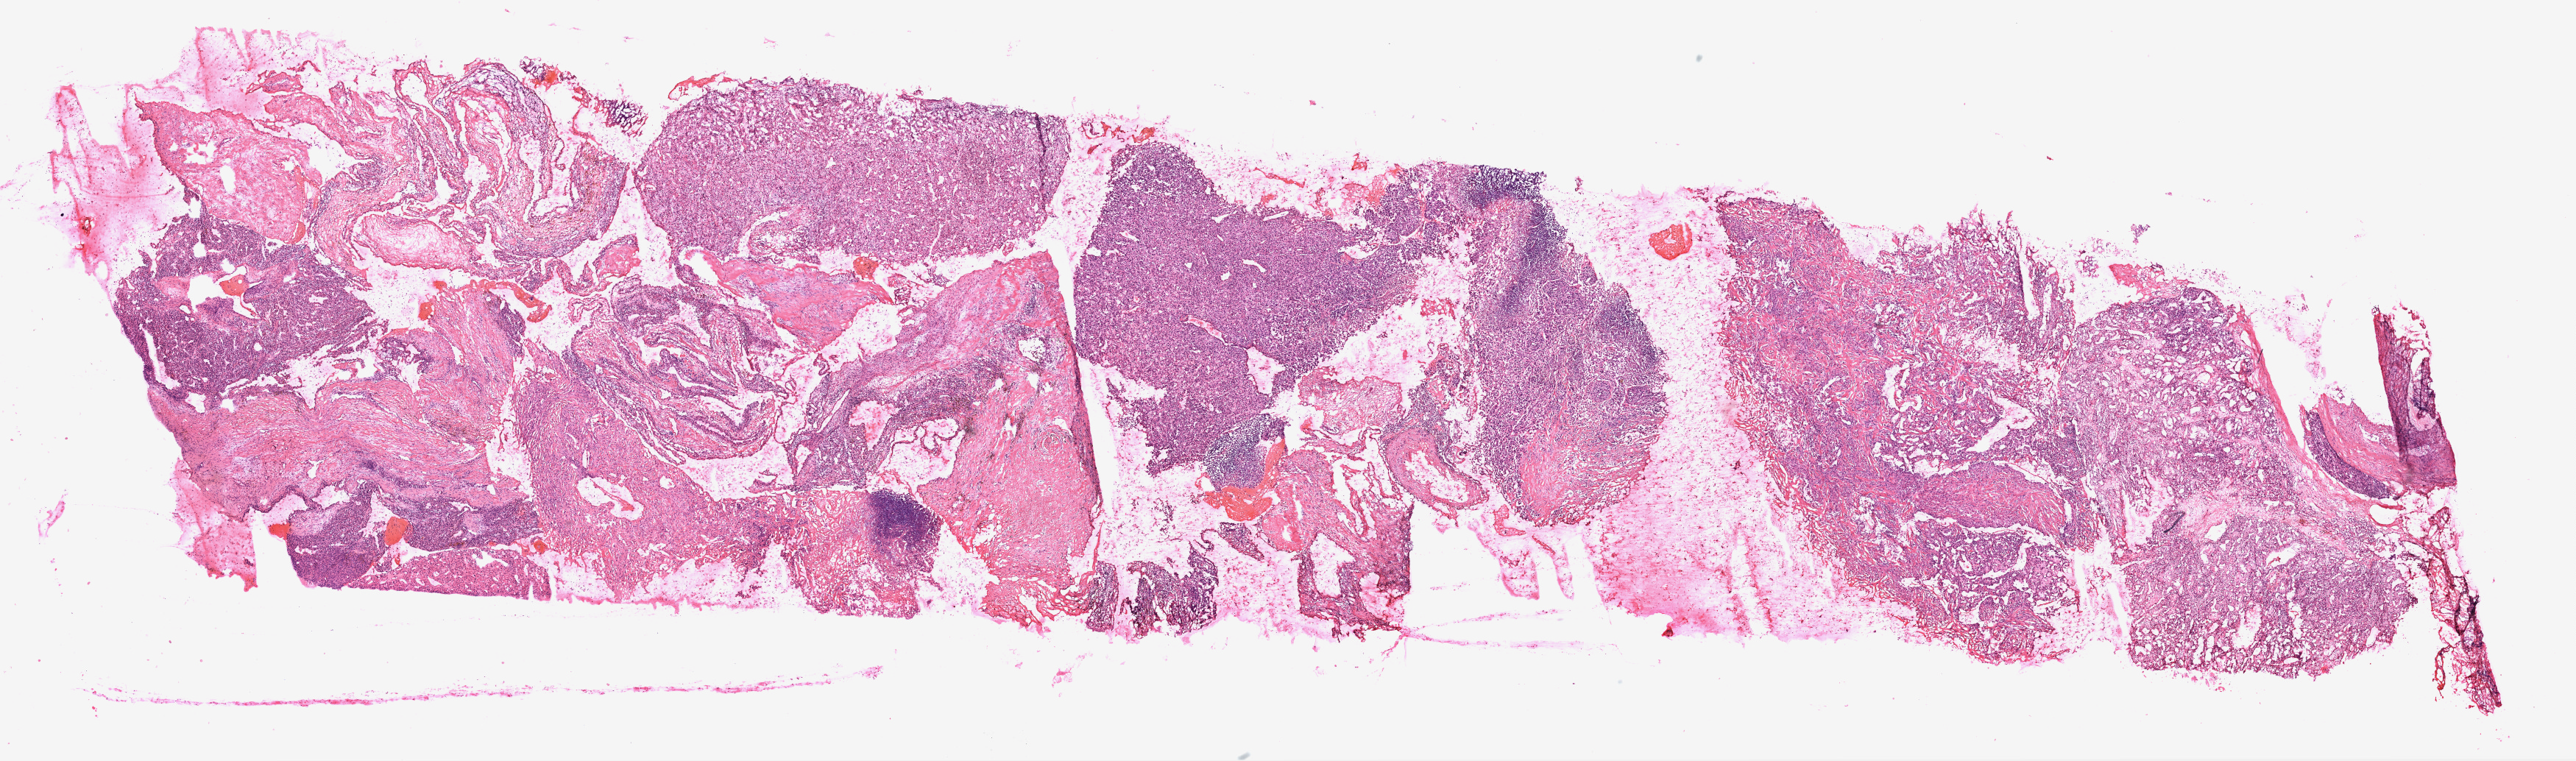
Digitized H&E-stained tissue section (whole slide) — whole scanned area (about 28.1 x 8.3 mm, from a 20x scan) shown as a low-resolution overview. Frozen section from the top of the tissue portion. Sample: primary tumour, kidney. Male, age 42 years at initial diagnosis. Histologic grade: G3 (poorly differentiated). Slide review estimates, as recorded: tumour cells 68%, tumour nuclei 75%, normal cells 0%, stromal cells 30%, necrosis 2%.
Pathologic diagnosis: Clear cell adenocarcinoma, NOS. AJCC pathologic stage: IV. Lymph nodes positive (case pathology): 0 of 14 examined.